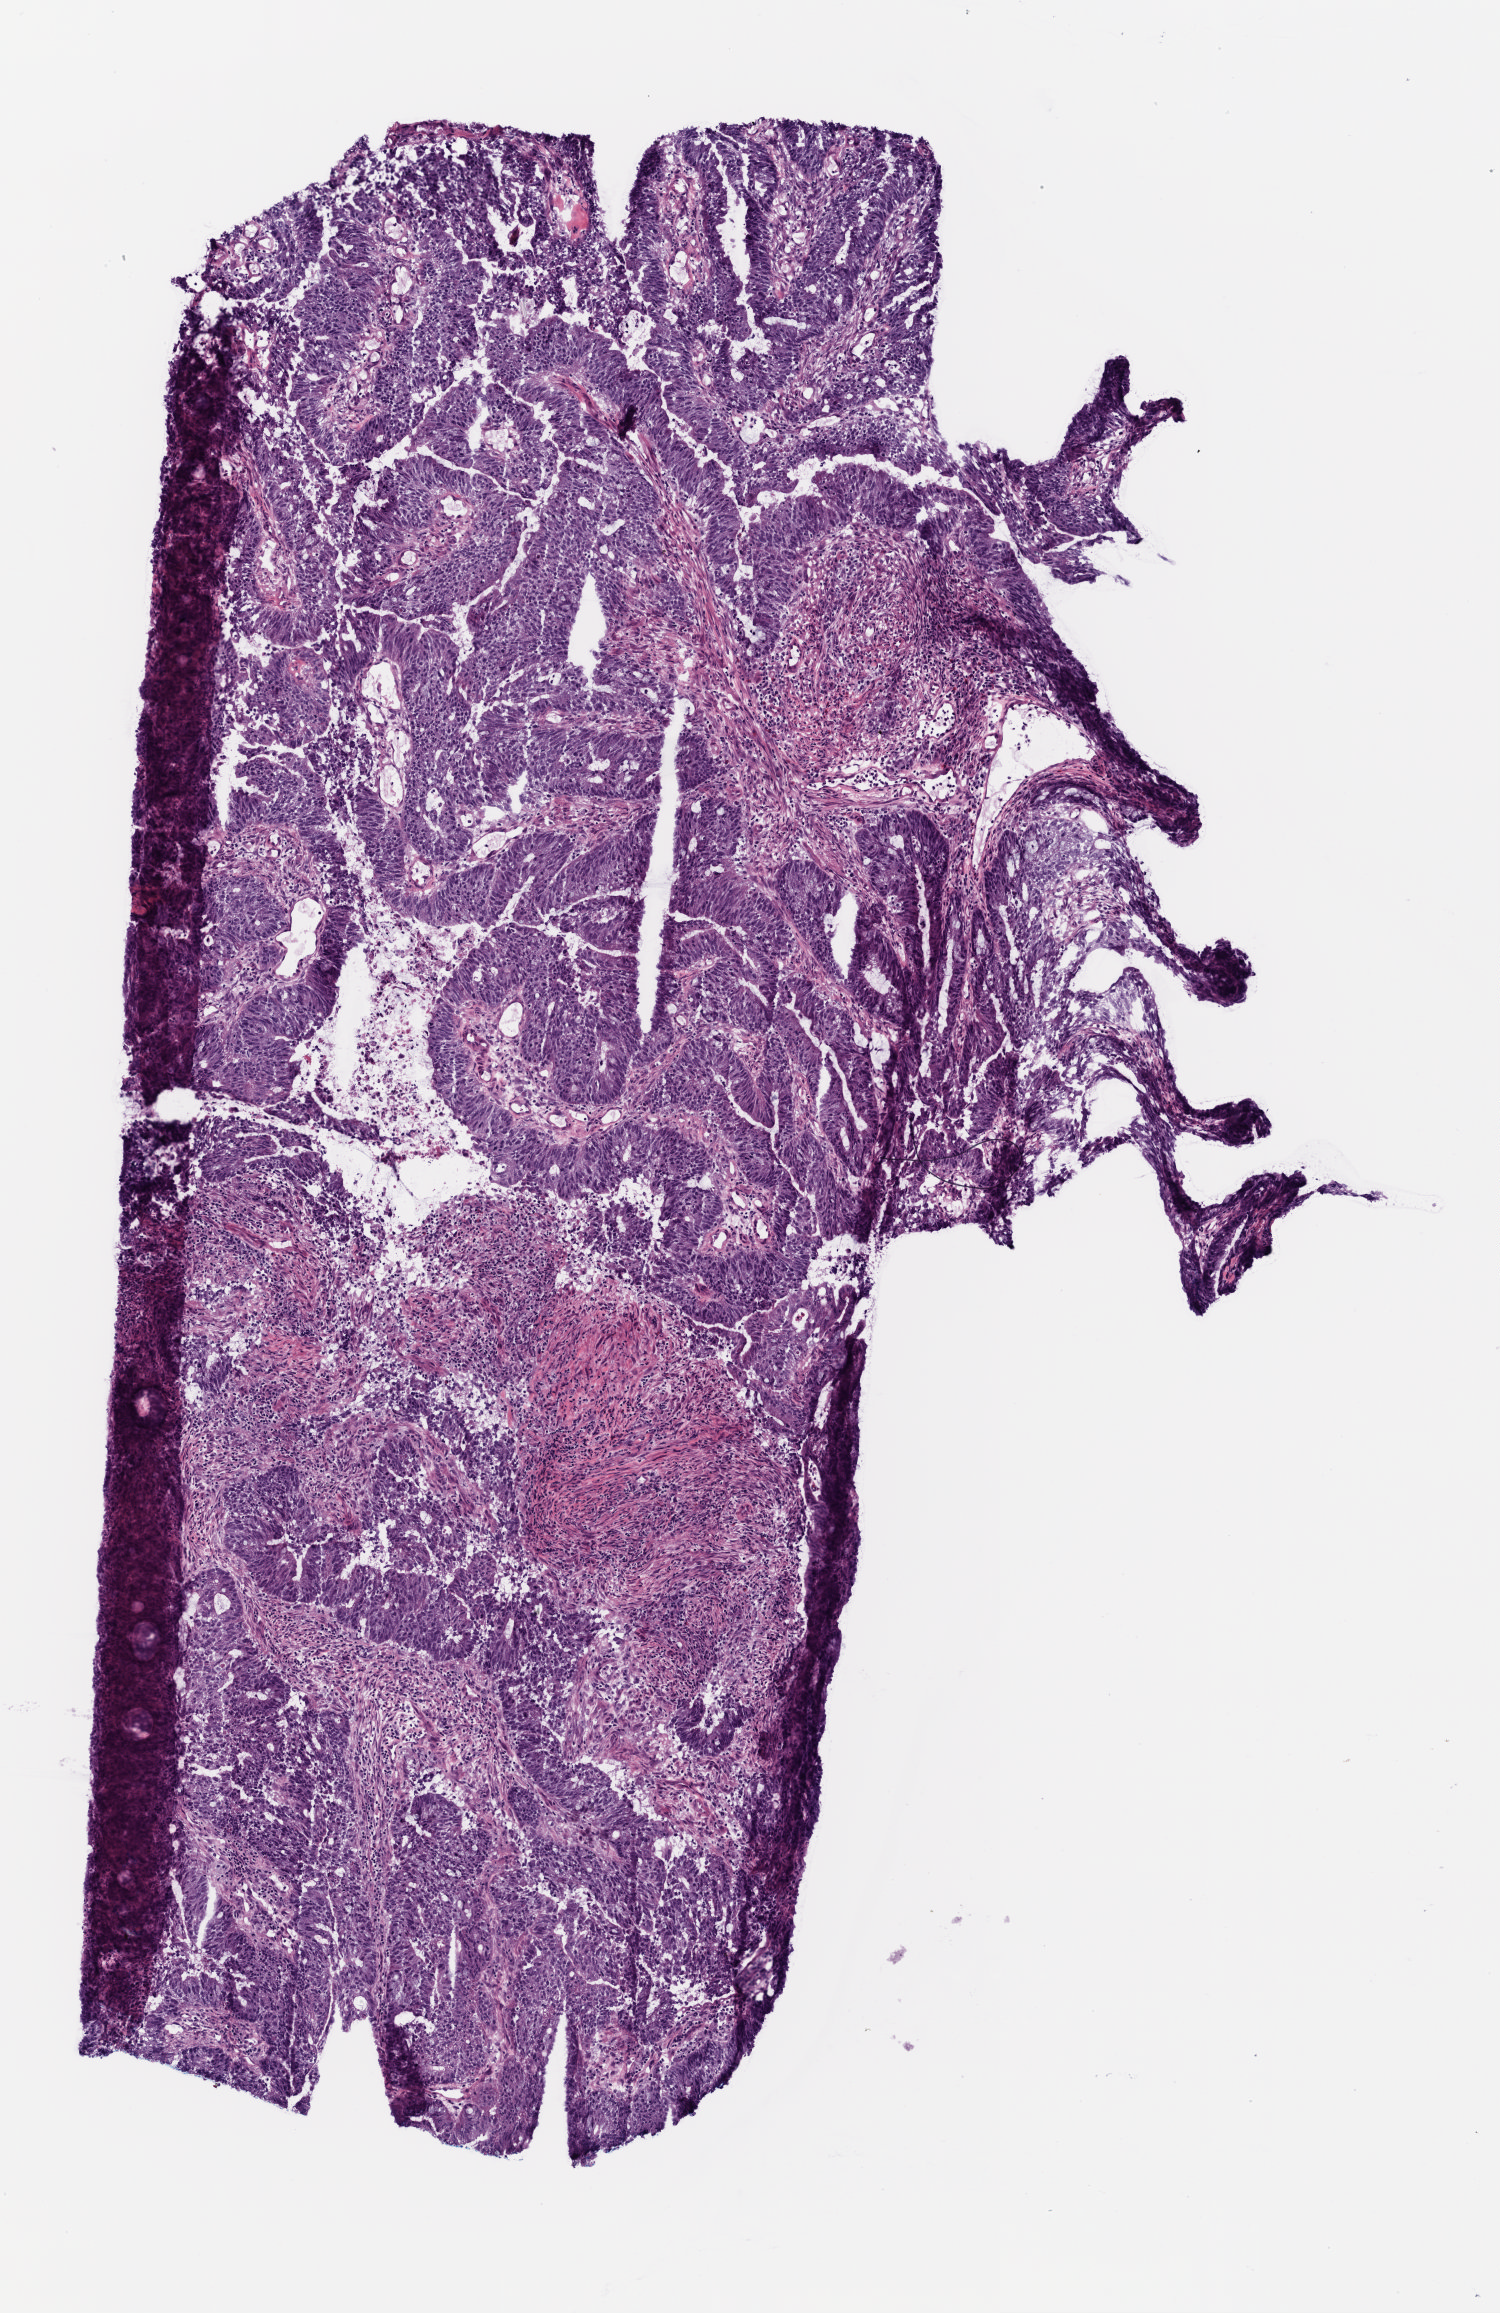
Hematoxylin and eosin (H&E) stained whole-slide image, a low-resolution overview of the entire scanned area, about 3.0 x 4.6 mm; frozen section; colon, primary tumour sample. Patient: male, age at initial diagnosis 65 years. Slide review estimates, as recorded: tumour cells 70%, tumour nuclei 80%, normal cells 0%, stromal cells 30%, necrosis 0%. Infiltration values recorded for this section: lymphocyte infiltration 3%.
Diagnosis: Adenocarcinoma, NOS (sigmoid colon).